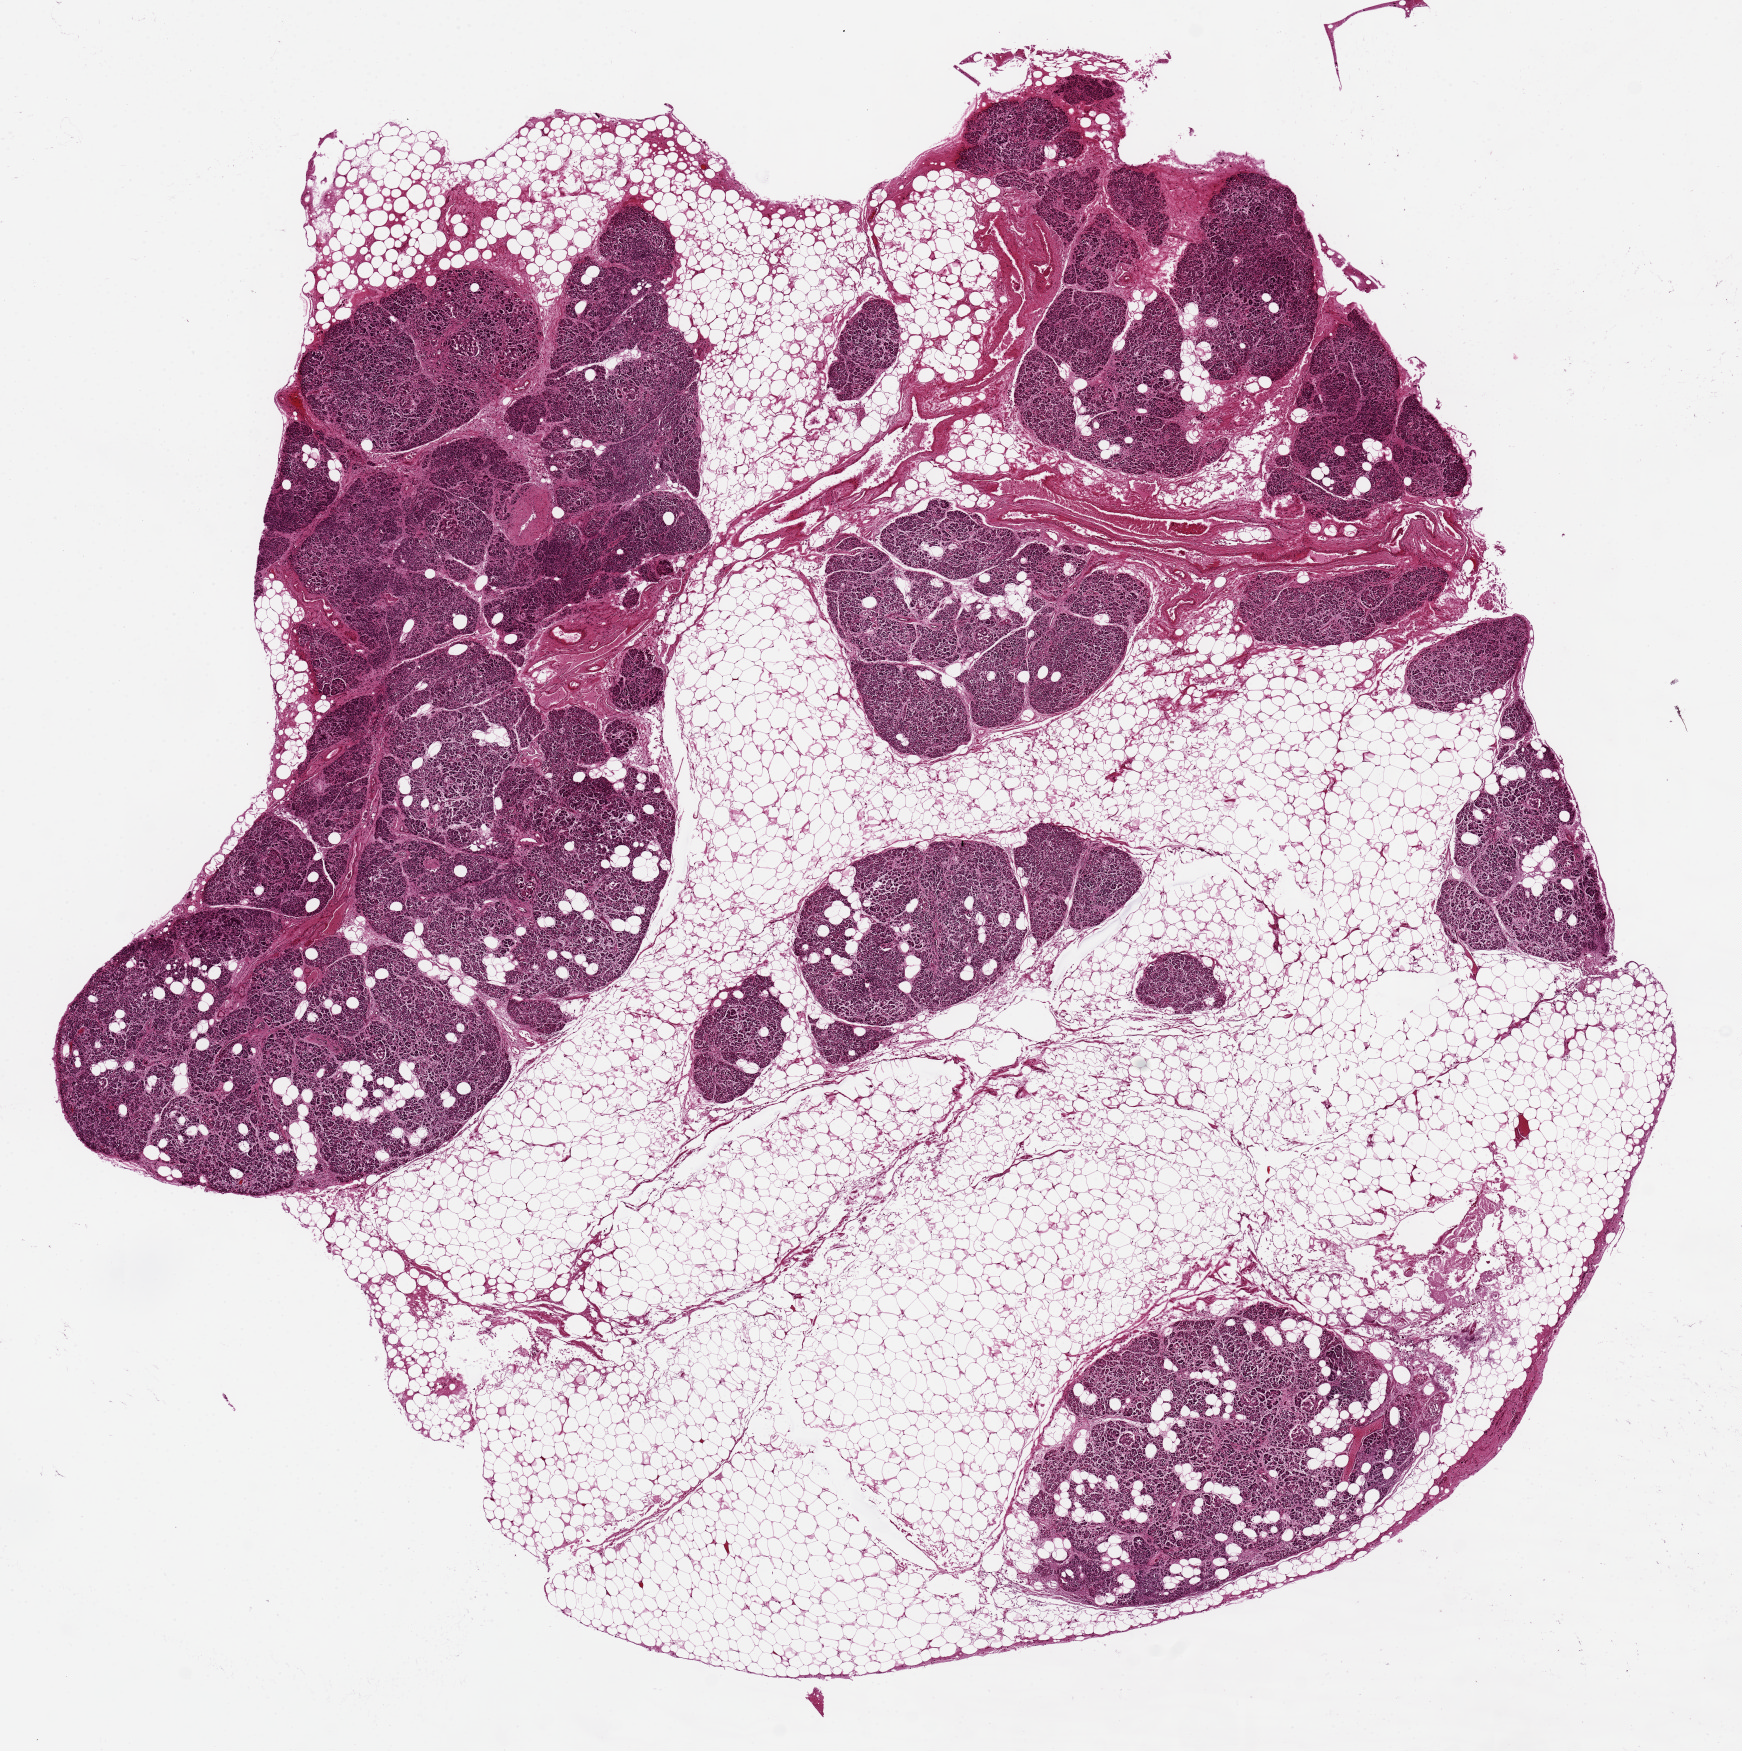
Digitized H&E-stained section, brightfield — whole scanned area (about 13.8 x 13.9 mm) shown as a low-resolution overview. PAXgene-fixed paraffin-embedded (PFPE) section. Section of pancreas (target tissue). Donor tissue sample. Donor sex: female.
Reviewer comment on this tissue sample: One piece 12.9x12.5mm. 50% is fat.